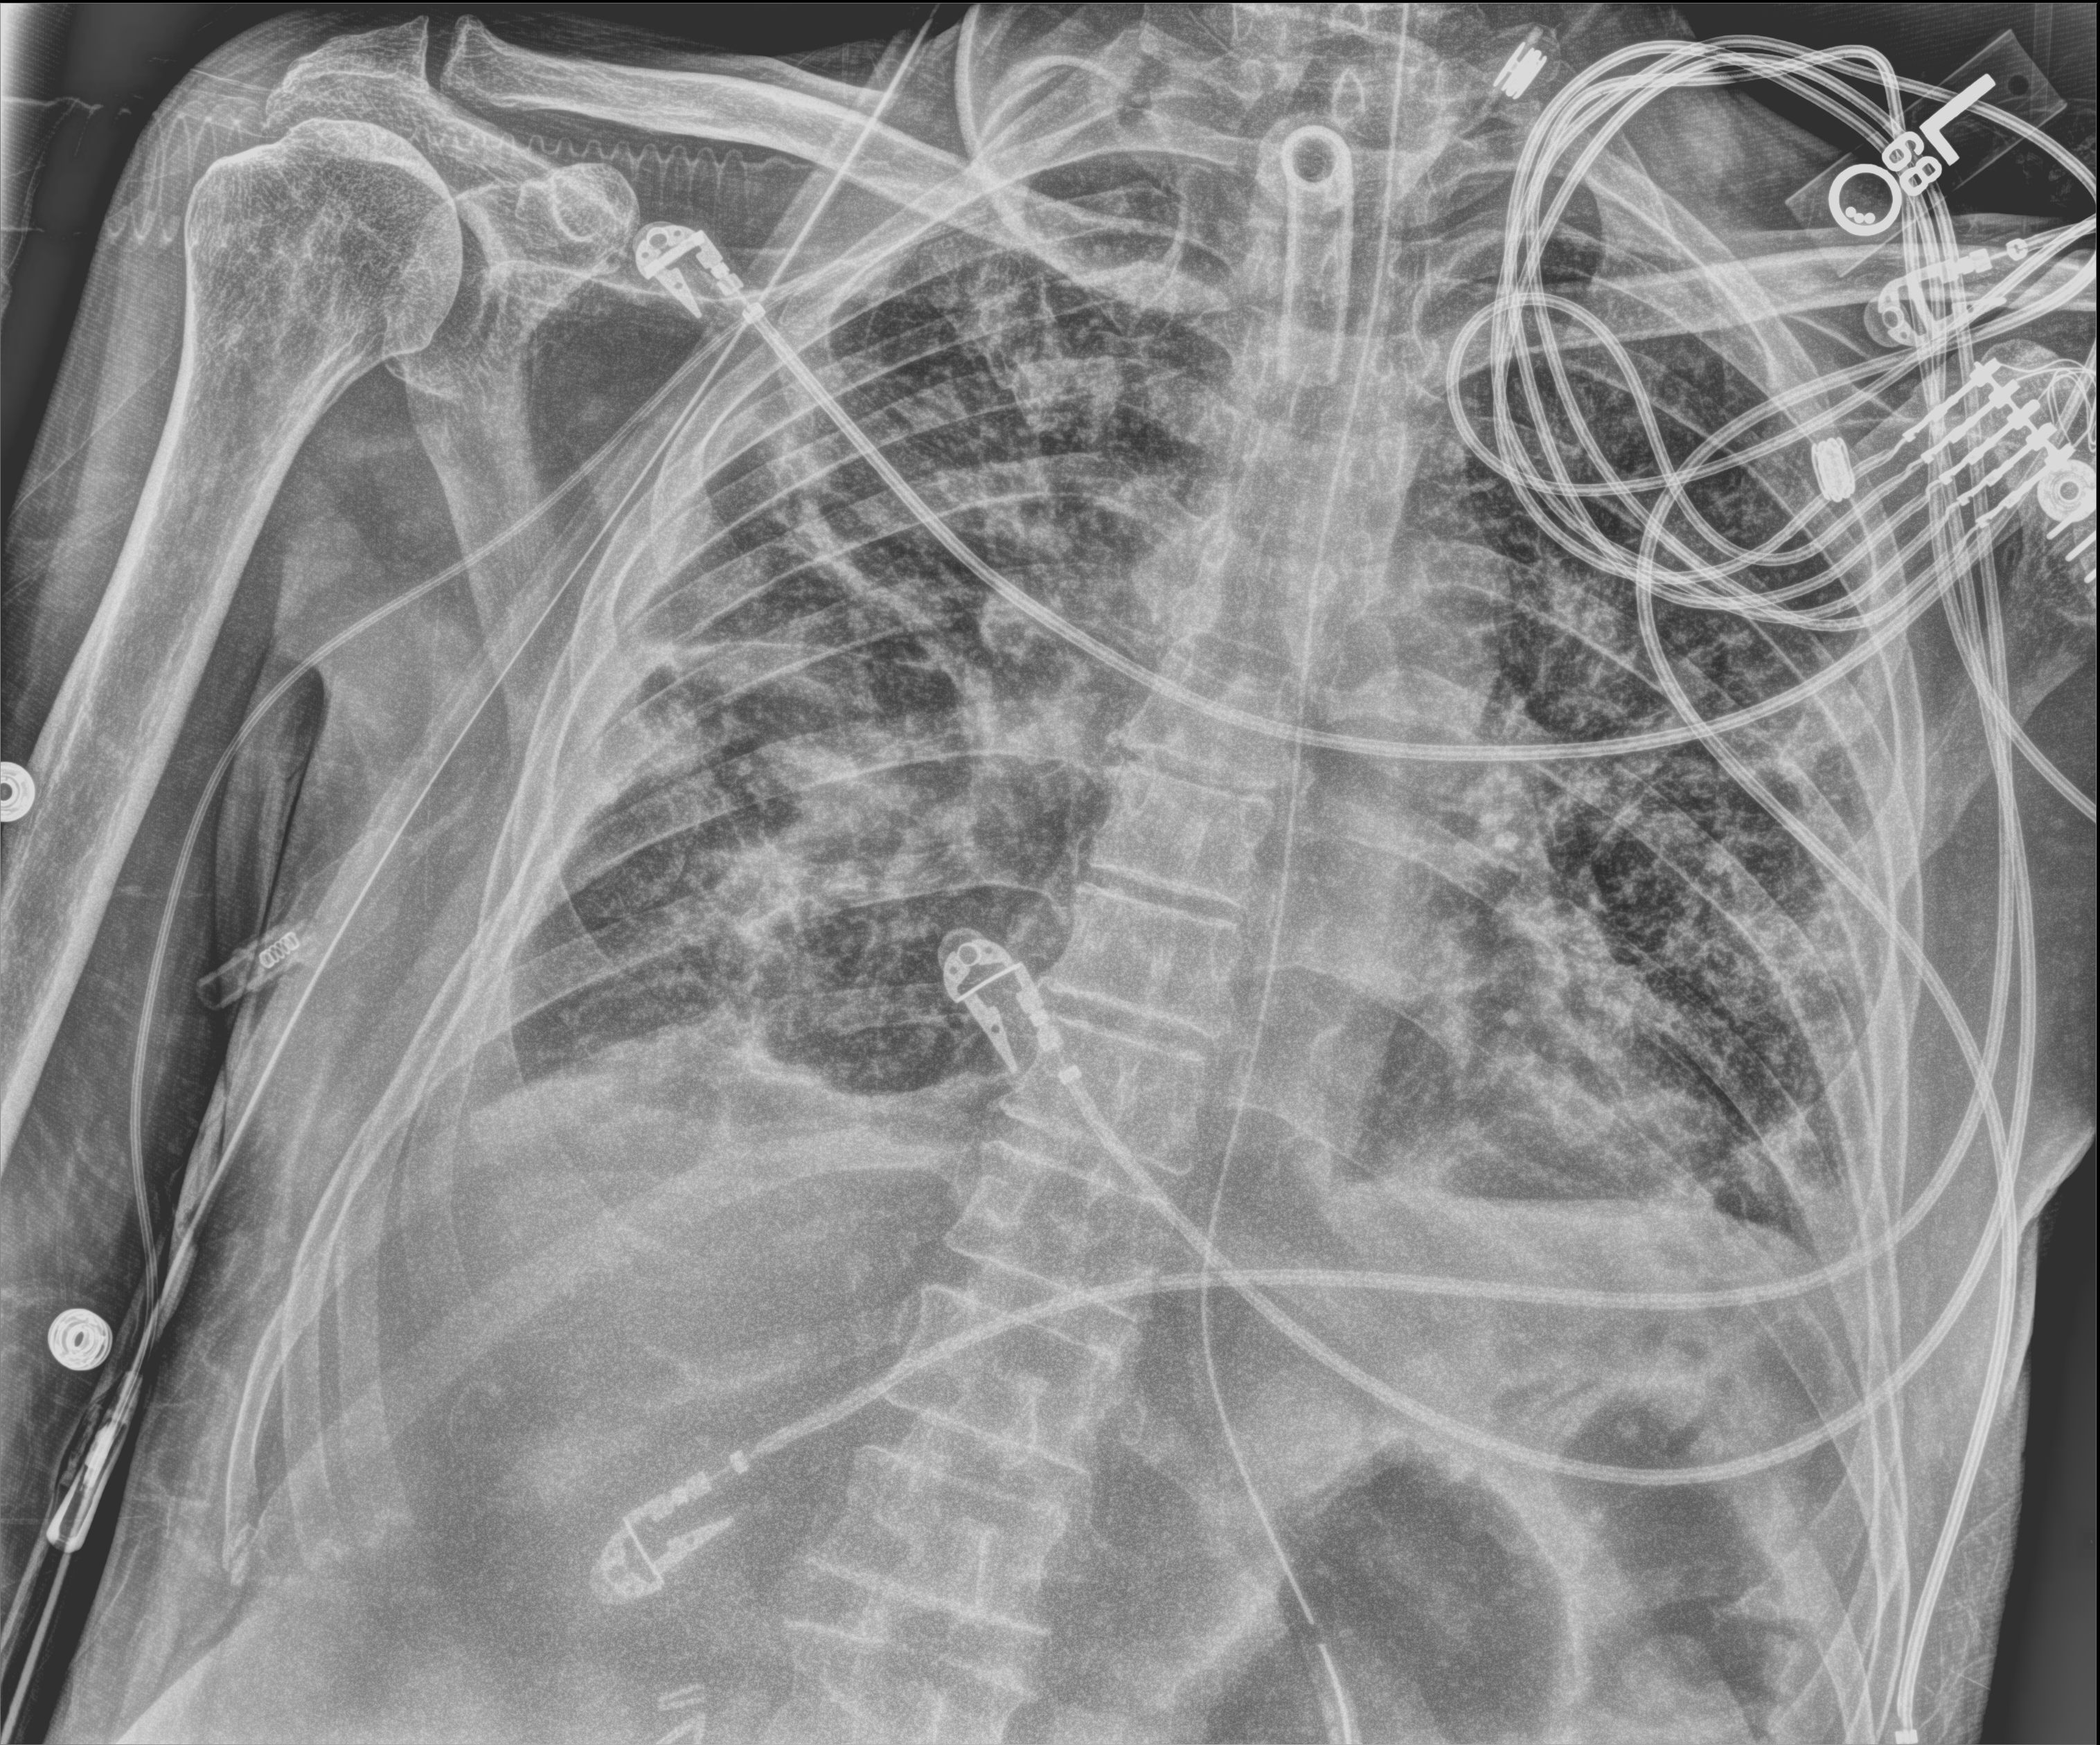
Chest X-ray (portable), anteroposterior (AP) projection. Male patient hospitalised with COVID-19, age 75–90 years.
Hospital-stay facts (about this admission, not read from this image; timing relative to this image not recorded):
- hypertension (admission record): no
- mechanically ventilated during this hospital stay: yes